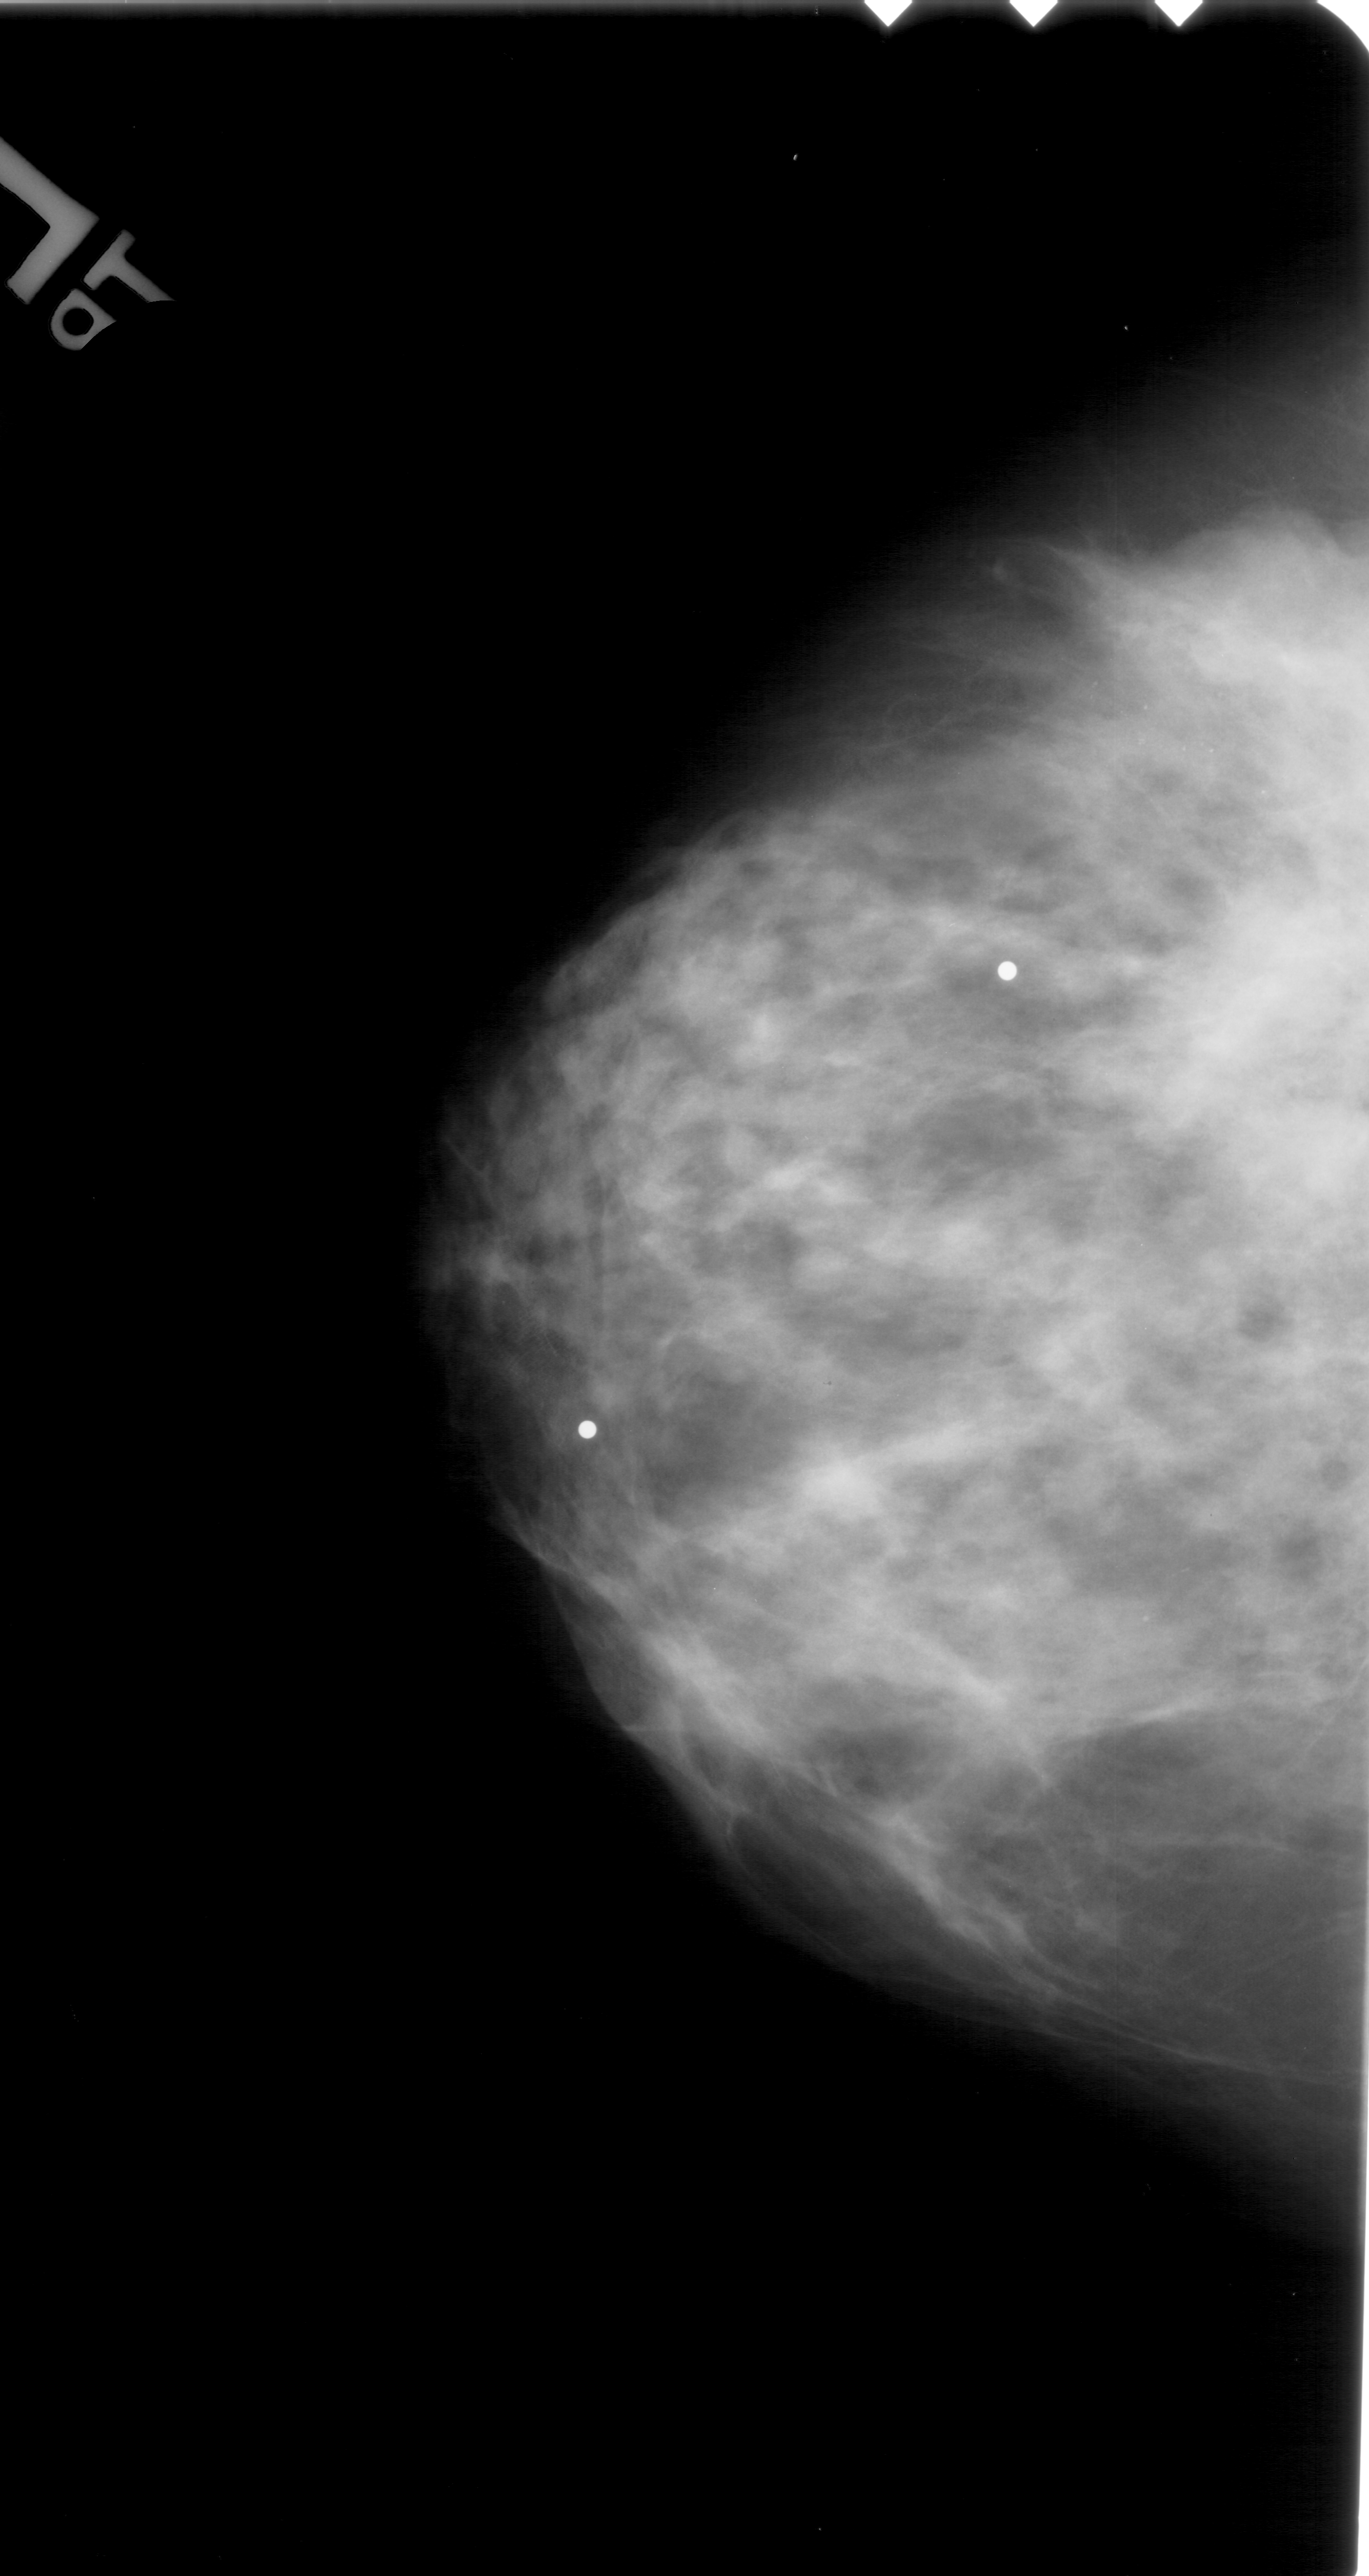
Digitized screen-film mammogram. Left breast. Craniocaudal (CC) view. Breast composition: extremely dense (BI-RADS density category 4 of 4). 1369 × 2576 image matrix.
Marked abnormalities (boxes around the expert regions of interest):
- calcifications, morphology amorphous, distribution clustered; BI-RADS assessment category 4; subtlety rating 1 on a 1 (subtle) to 5 (obvious) scale; pathology (as recorded): malignant: bounding box [x1, y1, x2, y2] px = [1063, 649, 1314, 819]